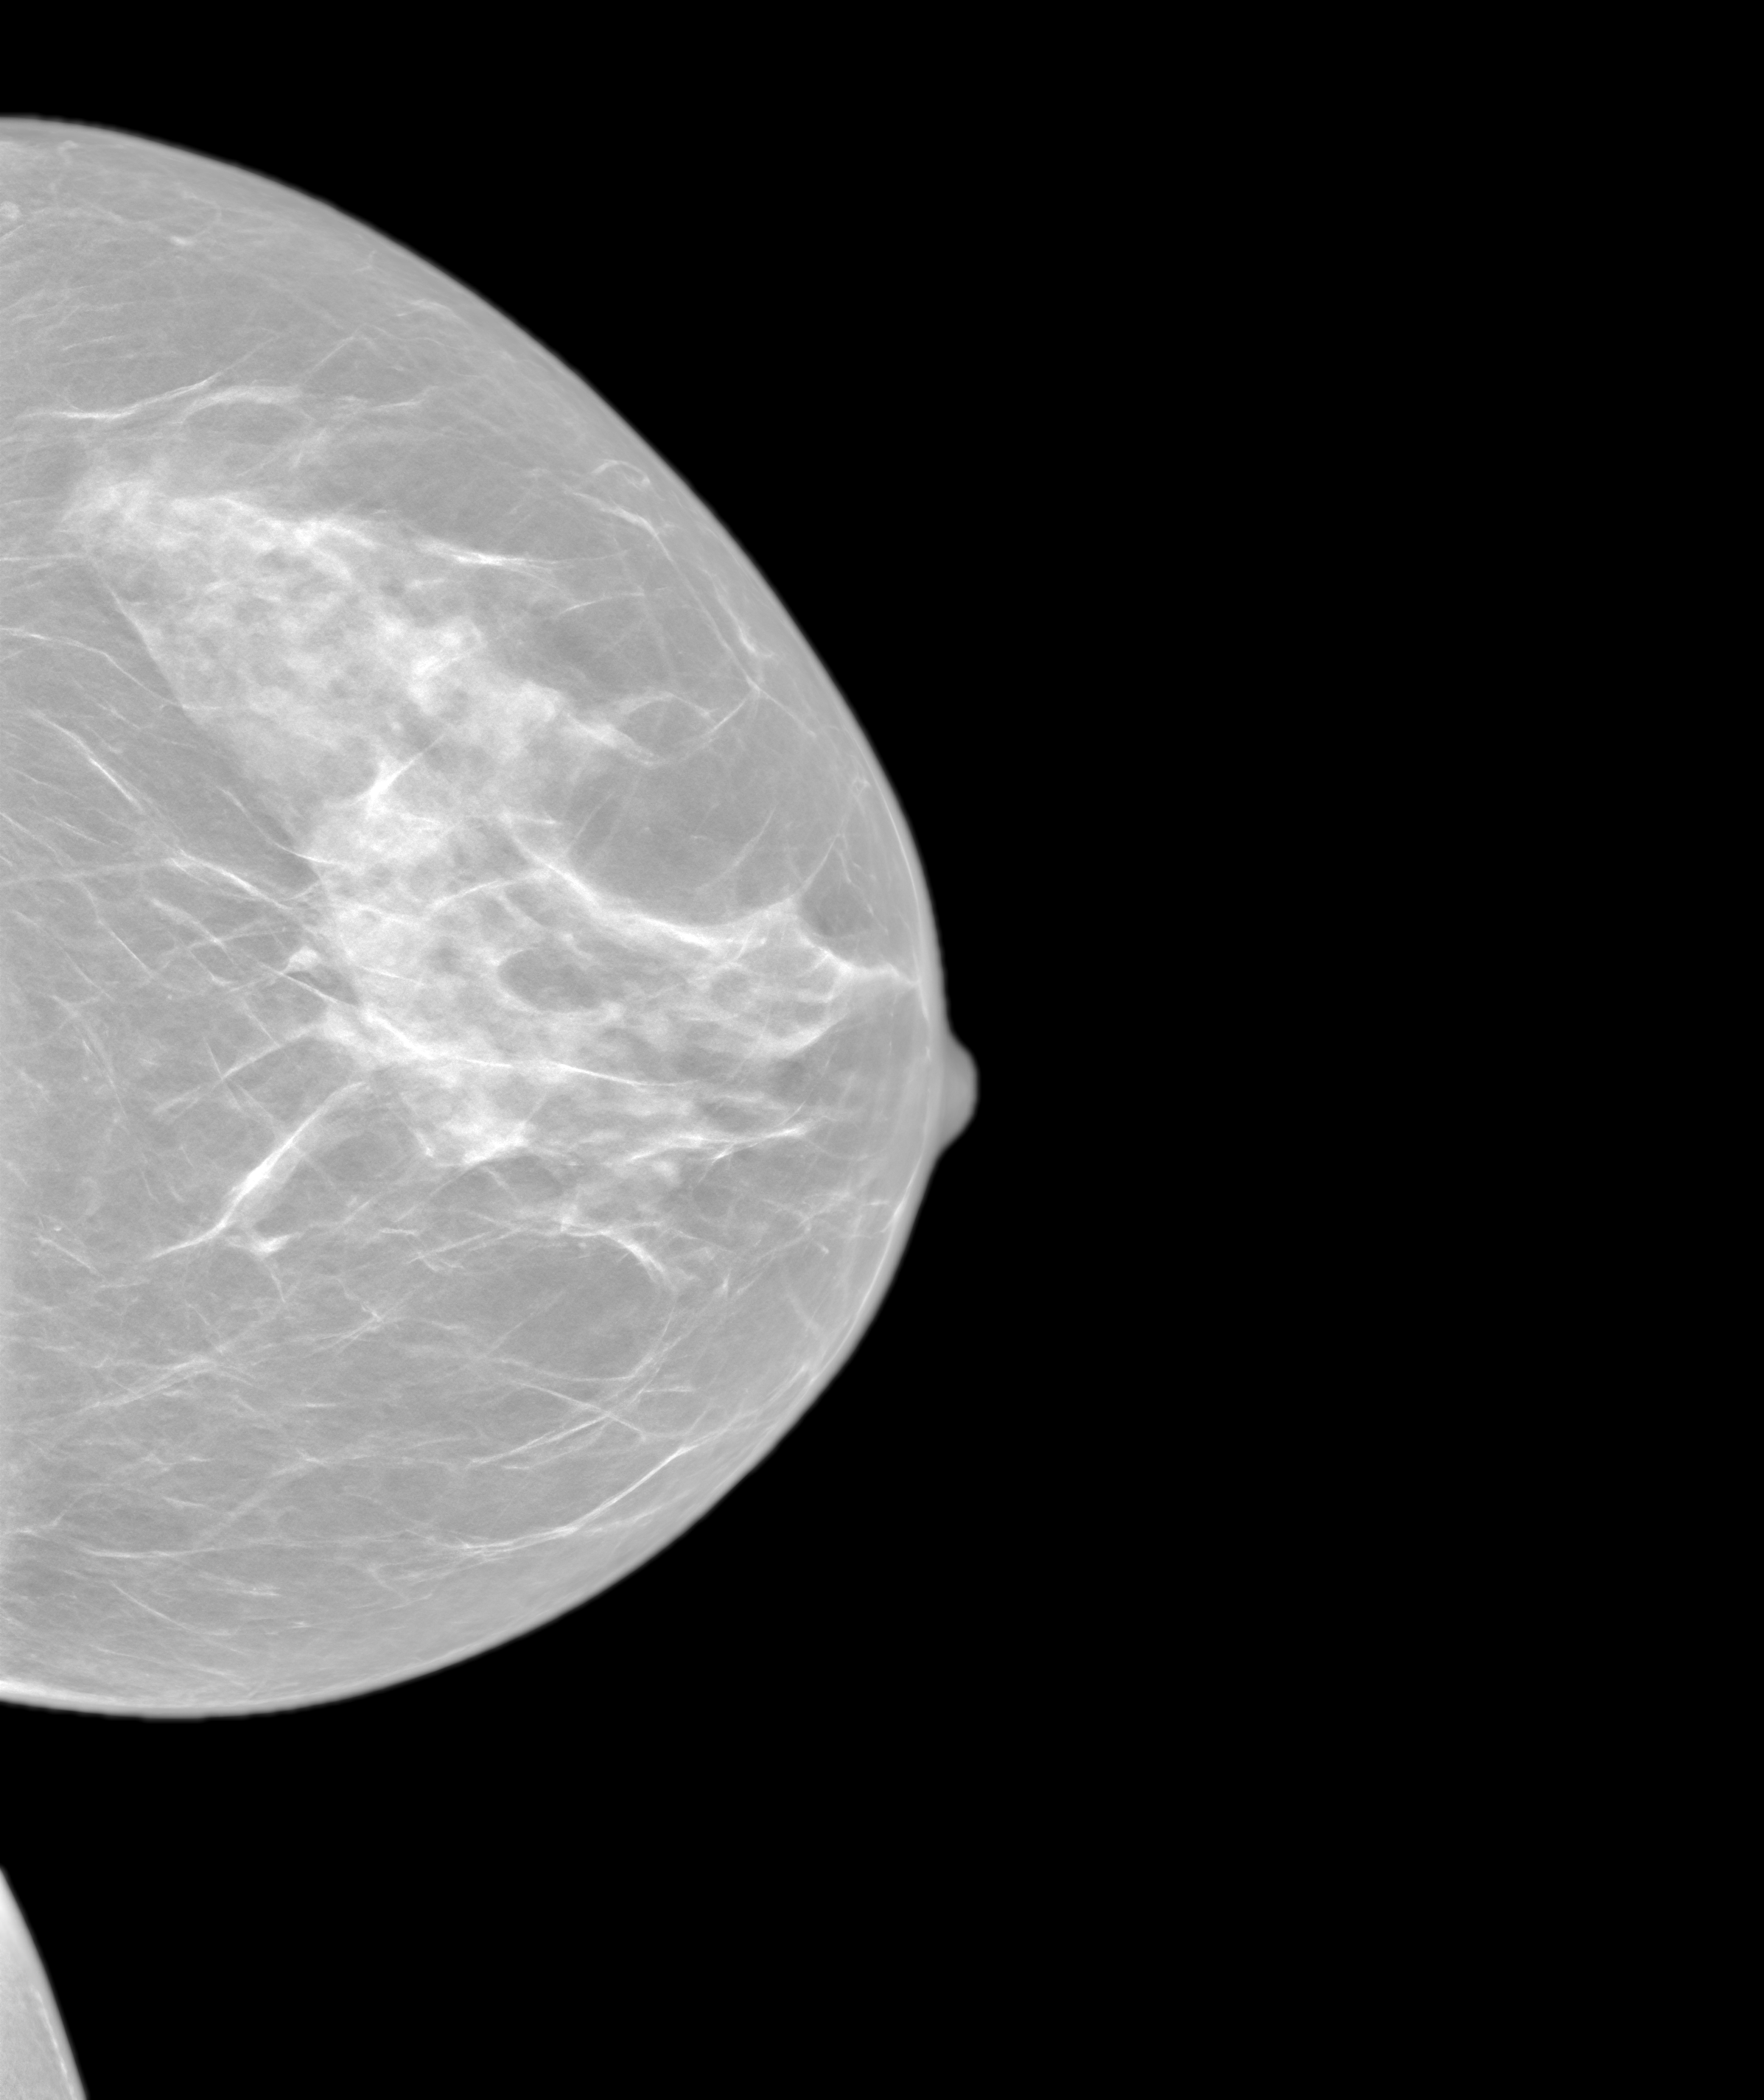
Synthetic 2-D view generated from a tomosynthesis acquisition (not an FFDM exposure), left breast, cranio-caudal projection, screening examination. Female patient, age 56 years.
BI-RADS breast density category at the screening exam (both breasts, scale 1–4): 3. Final BI-RADS assessment for this screening round (tomosynthesis exam, both breasts): category 1. Recall: no recall after this screen.